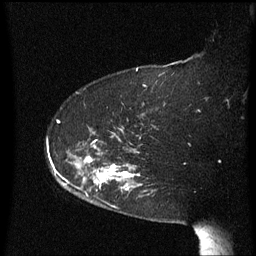
Breast MRI (dynamic contrast-enhanced), one sagittal slice. Dynamic contrast-enhanced series, image 2 of 3 at this slice position (ordered by acquisition). 1.5 T. TE 4.2 ms, TR 8.4 ms. 2.3 mm slice thickness. 256 × 256 image matrix. Patient: female, 63 years. From the clinical record (not read from this slice): setting: breast cancer imaged before/during neoadjuvant chemotherapy; receptor status: HER2-positive.
Structures marked on this image (semi-automatically segmented with operator editing):
- analysis volume of interest (the breast-tissue region the enhancement analysis was run in; not a lesion): bounding box [x1, y1, x2, y2] px = [71, 144, 143, 207]
- tumour enhancement mask (voxels above the 70 % enhancement threshold inside the analysis volume of interest): [85, 158, 140, 191]